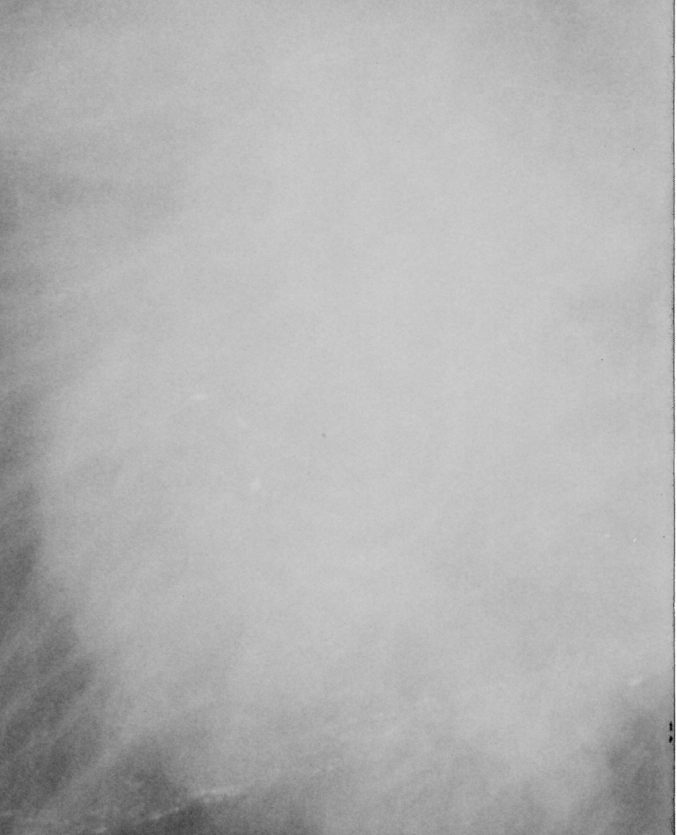
Region of interest cut from a scanned film mammogram (one marked finding), right breast, MLO view, BI-RADS breast density category 1 (scale 1–4).
Marked abnormality: mass, shape irregular, margins spiculated; BI-RADS assessment category 4; pathology (as recorded): malignant.